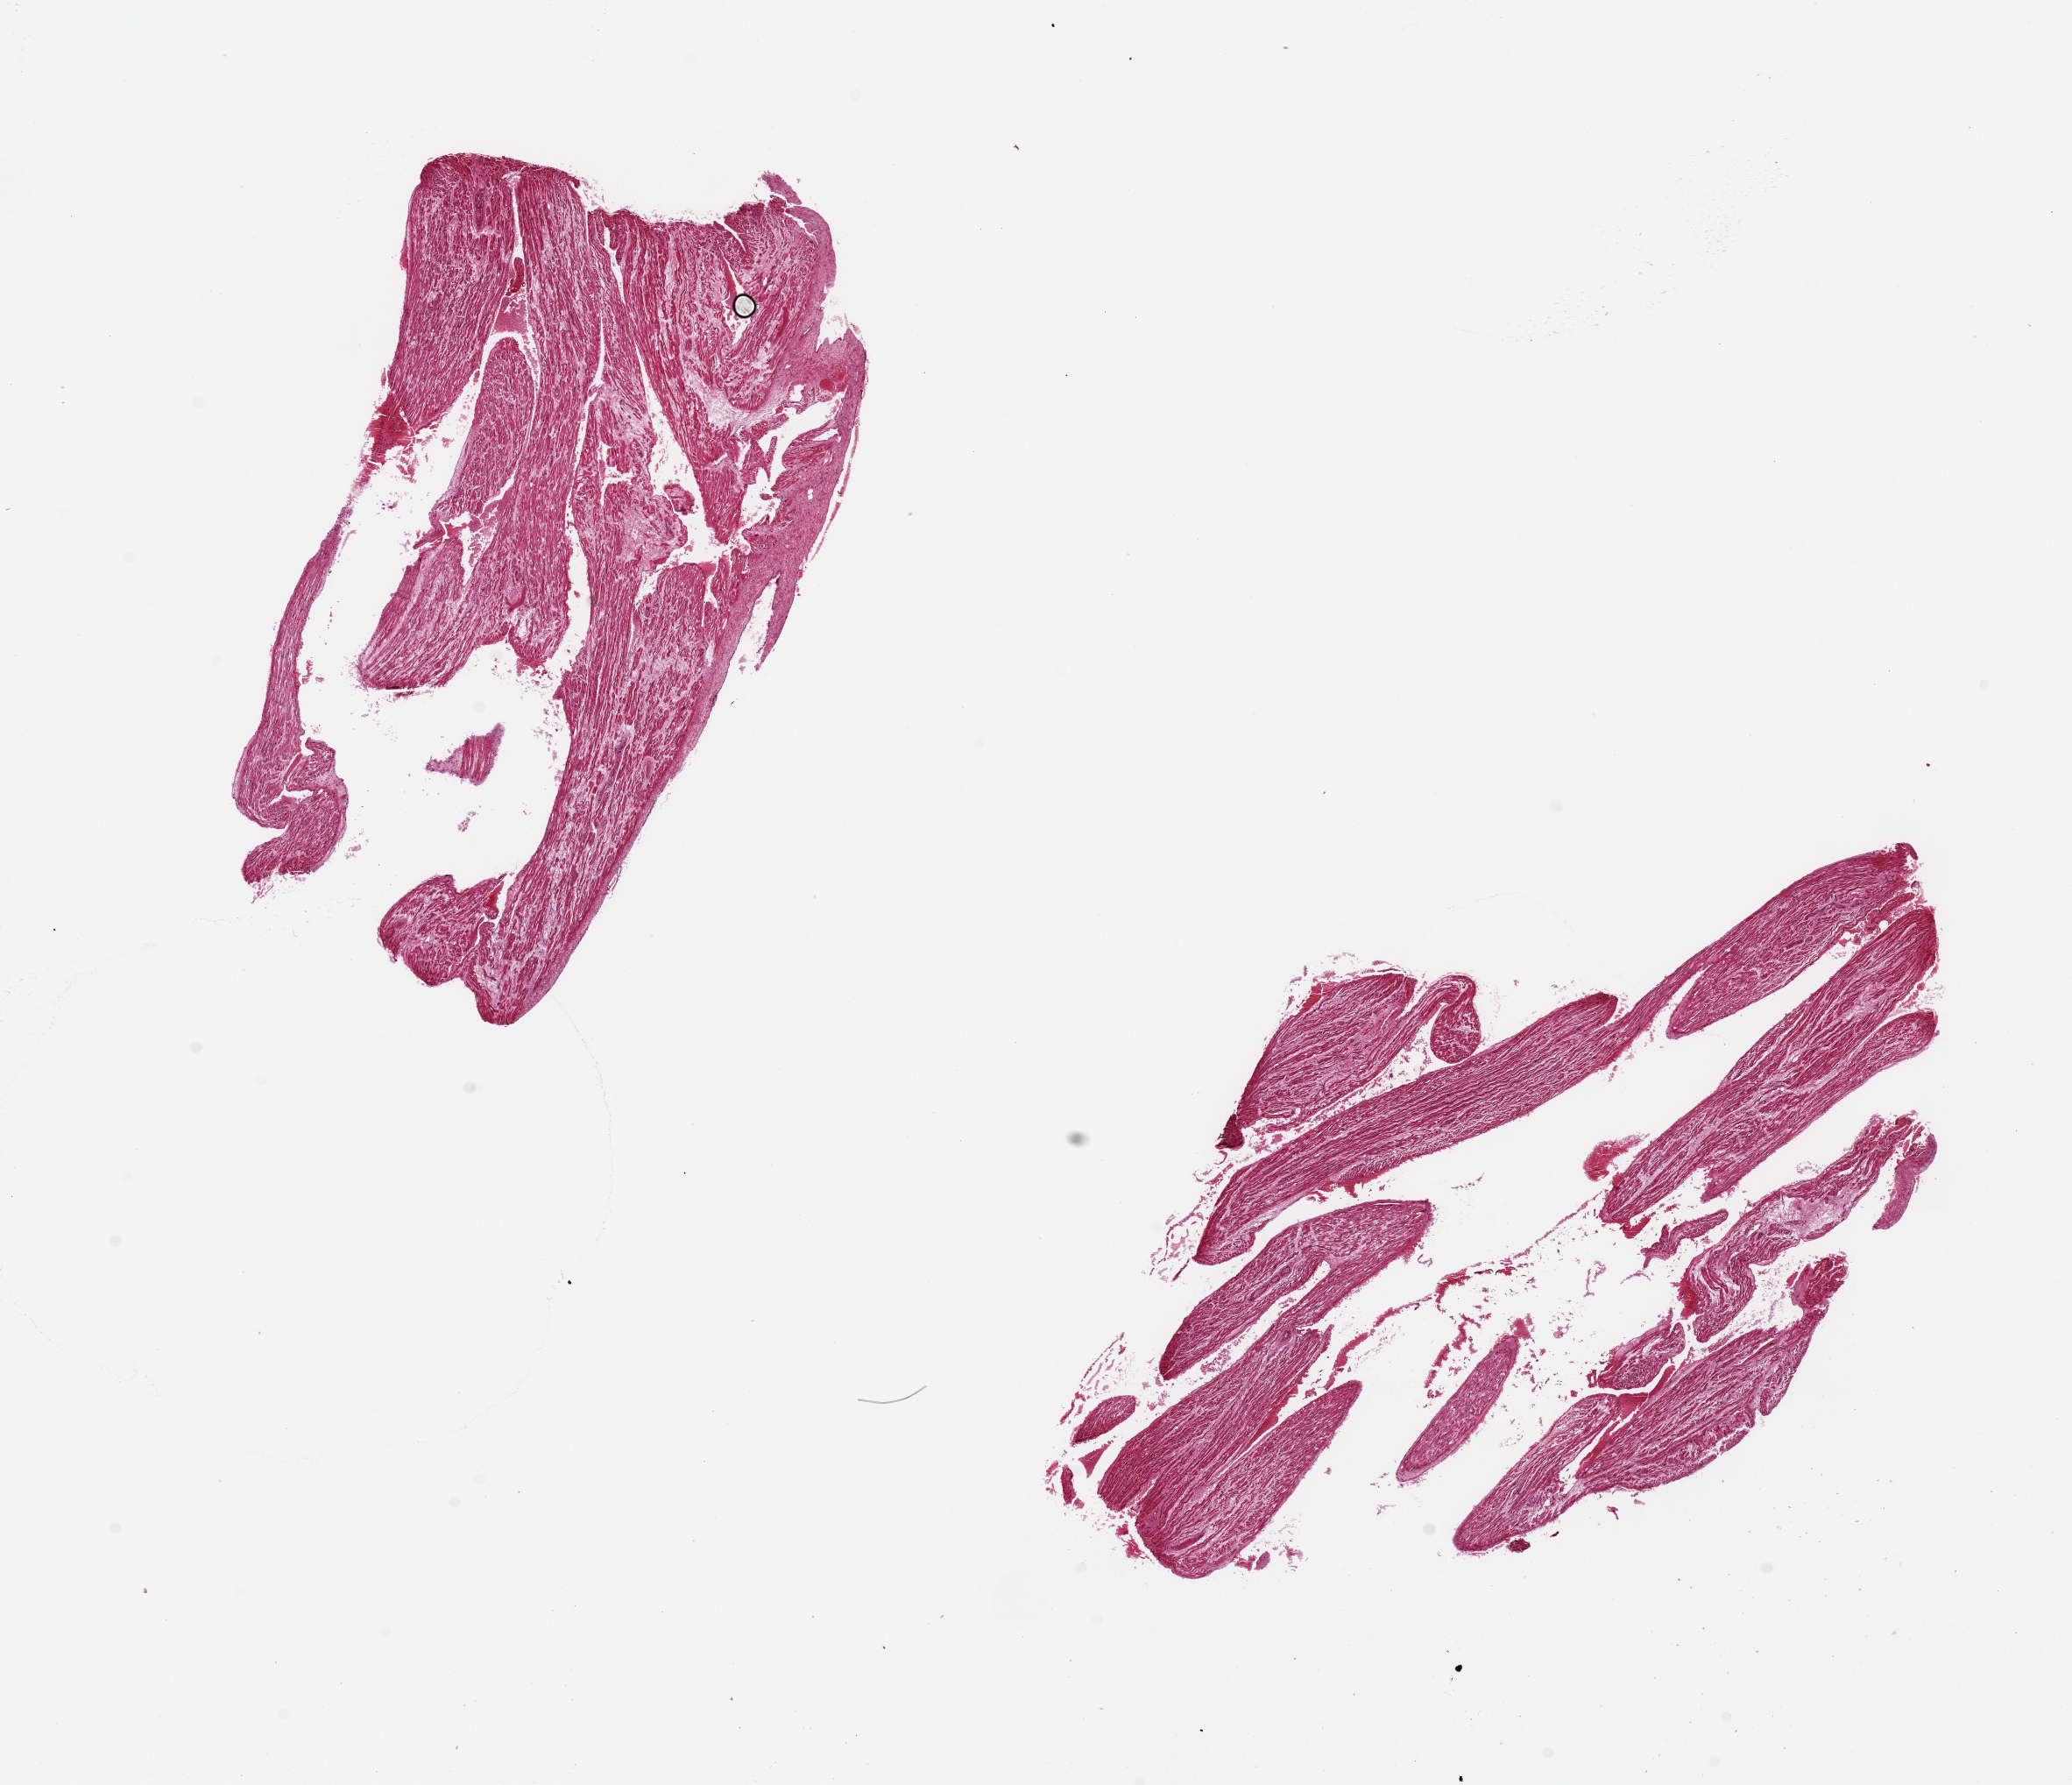
Digitized hematoxylin and eosin (H&E)-stained section, brightfield, shown as a low-resolution overview of the whole scanned area (about 18.7 x 16.1 mm, acquisition: 20x scan). PAXgene-fixed, paraffin-embedded tissue. Section of auricular appendage (target tissue). Donor tissue sample.
Pathologist's review note for this sample: 2 pieces, 8.5x5 & 8x4mm; appears edematous.